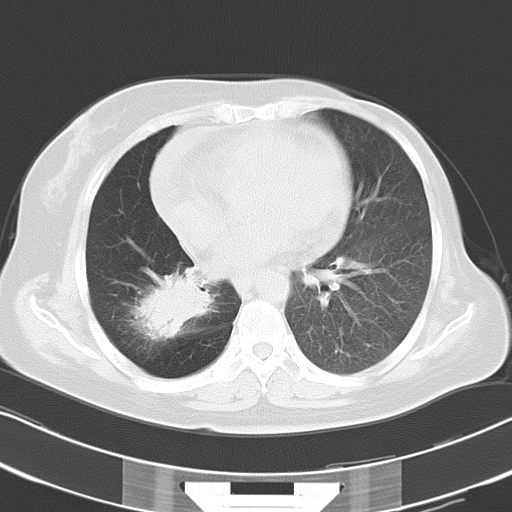
Chest CT, one axial slice. Slice 14 of 30 in the series (ordered by position). 120 kVp. Lung window (W 1500 / L -600 HU). 512 × 512 image matrix, field of view 331 × 331 mm. Patient: female, 53 years. From the clinical record (not read from this slice): clinical TNM (as recorded): T2b N1 M0.
Outlined on this slice (rectangle marked by the reading radiologist):
- lung tumour (recorded histology: adenocarcinoma): bounding box [x1, y1, x2, y2] px = [125, 267, 216, 343]